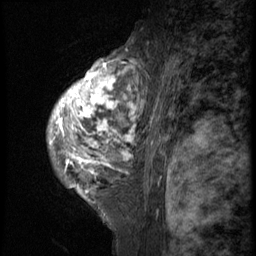
Breast MRI (dynamic contrast-enhanced), one sagittal slice; slice 41 of 58 in the series (ordered by position); 3 images stored at this slice position (order not interpretable as contrast timing); 1.5 T; TE 4.2 ms, TR 9 ms; 2.5 mm slice thickness; 256 × 256 image matrix, field of view 180 × 180 mm. Female patient, age 50 years. From the clinical record (not read from this slice): setting: breast cancer imaged before/during neoadjuvant chemotherapy; receptor status: triple-negative.
Outlined on this slice (semi-automatic segmentation, software-assisted and operator-edited):
- analysis volume of interest (the breast-tissue region the enhancement analysis was run in; not a lesion): box from (x=48, y=48) to (x=131, y=214) px
- tumour enhancement mask (voxels above the 140 % enhancement threshold inside the analysis volume of interest): (x=51, y=60)–(x=131, y=198)